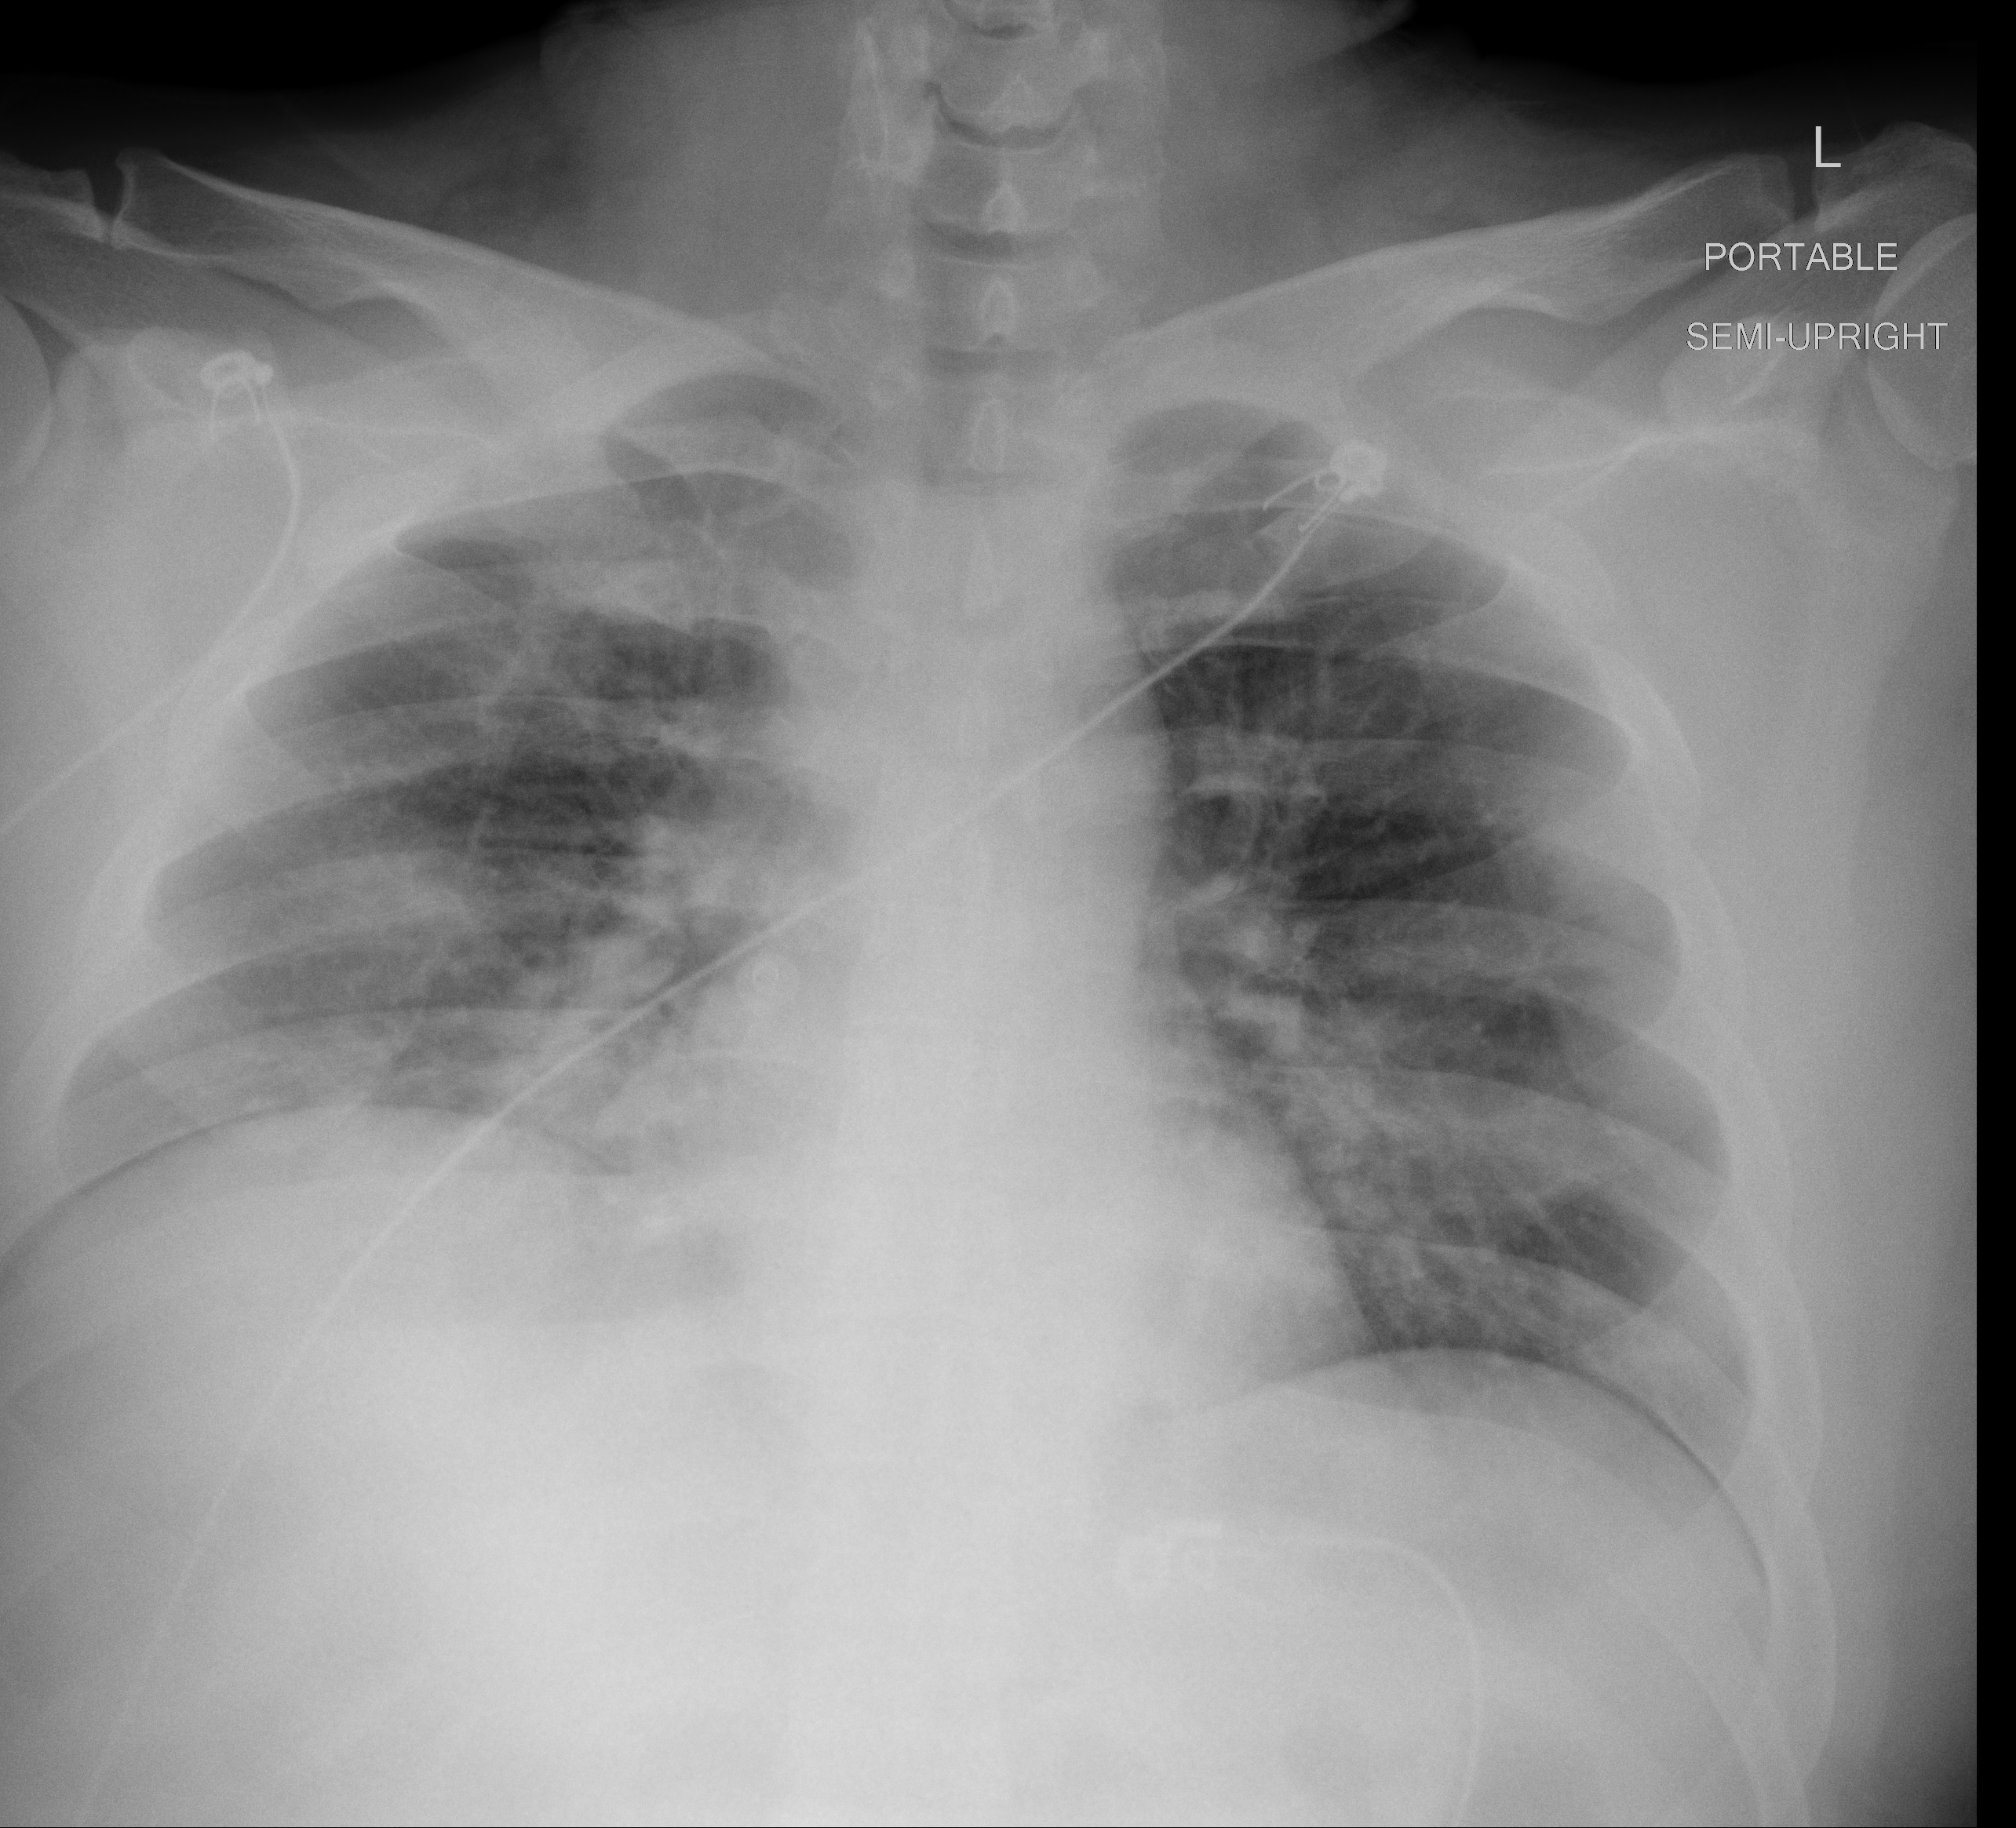
Chest radiograph, AP projection. Male patient, age 38 years; imaged 1 day after the COVID-19 diagnosis.
Radiologist key findings (as recorded): interval decrease in aeration of the lungs with stable to worsening bilateral lower lobe peribronchovascular airspace disease.